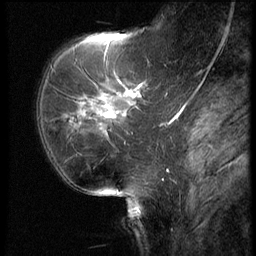
Breast MRI (dynamic contrast-enhanced), one sagittal slice; position 21 of 62 along the scan axis; 3 images stored at this slice position (order not interpretable as contrast timing); 1.5 T; TE 4.2 ms, TR 9 ms; 2.5 mm slice thickness; 256 × 256 image matrix, field of view 180 × 180 mm. Patient: female, 62 years. From the clinical record (not read from this slice): setting: breast cancer imaged before/during neoadjuvant chemotherapy; receptor status: HR-positive, HER2-negative.
Structures marked on this image (semi-automatic segmentation, software-assisted and operator-edited):
- analysis volume of interest (the breast-tissue region the enhancement analysis was run in; not a lesion): bounding box [x1, y1, x2, y2] px = [56, 62, 154, 155]
- tumour enhancement mask (voxels above the 140 % enhancement threshold inside the analysis volume of interest): [103, 93, 135, 118]